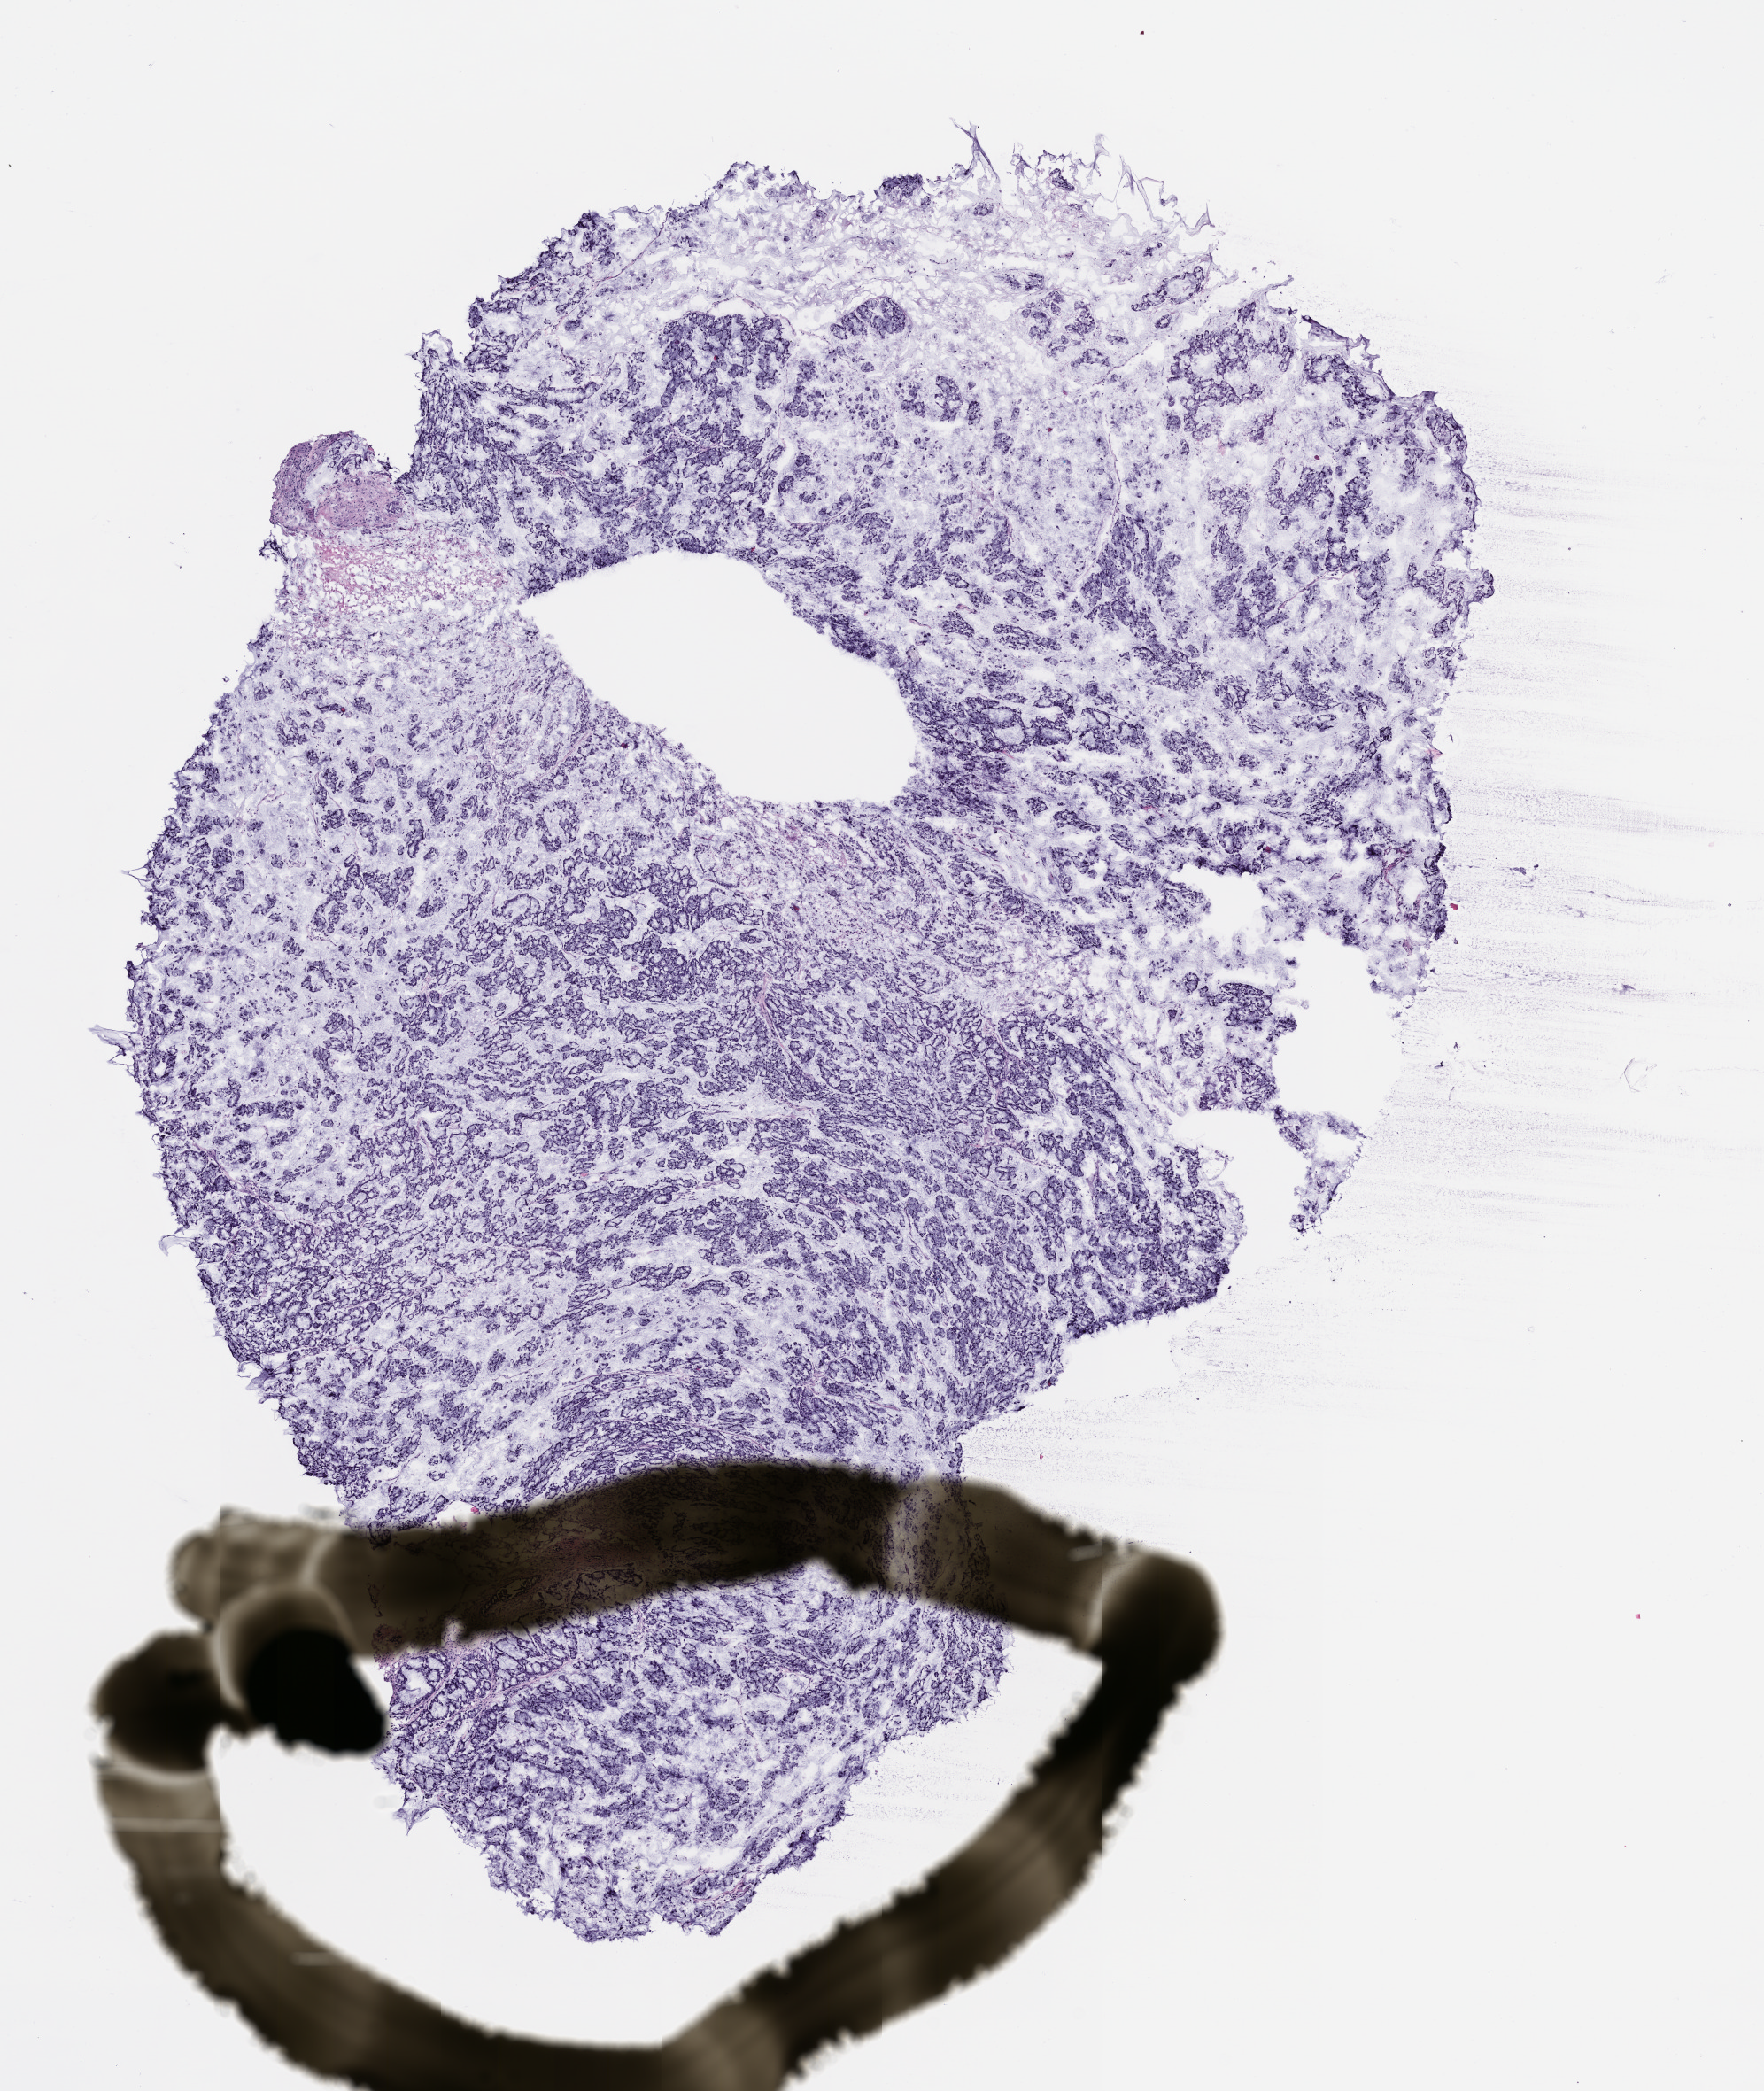
Whole-slide image, H&E: patient-derived xenograft (human tumor grown in a mouse), passage 1, shown as a low-resolution overview of the whole scanned area (about 8.0 x 9.5 mm). FFPE section. Tumor site category: colon.
Originating patient diagnosis: Colon Adenocarcinoma.